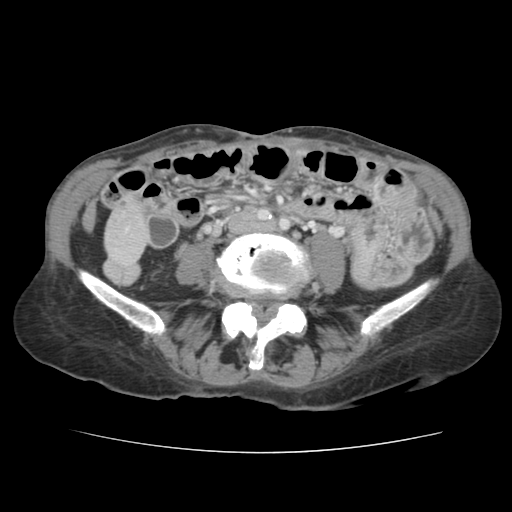
Contrast-enhanced abdominal CT, one axial slice. Position 15 of 136 along the scan axis. 120 kVp. Intravenous contrast given. Soft-tissue window (W 400 / L 40 HU). 2.5 mm slice thickness. 512 × 512 image matrix. Female patient, age 77 years. From the clinical record (not read from this slice): diagnosis: colorectal cancer liver metastases, imaged before liver resection; multiple liver metastases: yes; largest metastasis: 3 cm.
Outlined on this slice (expert manual segmentation):
- liver: bounding box (x1, y1, x2, y2) in pixels: (107, 204, 146, 273)